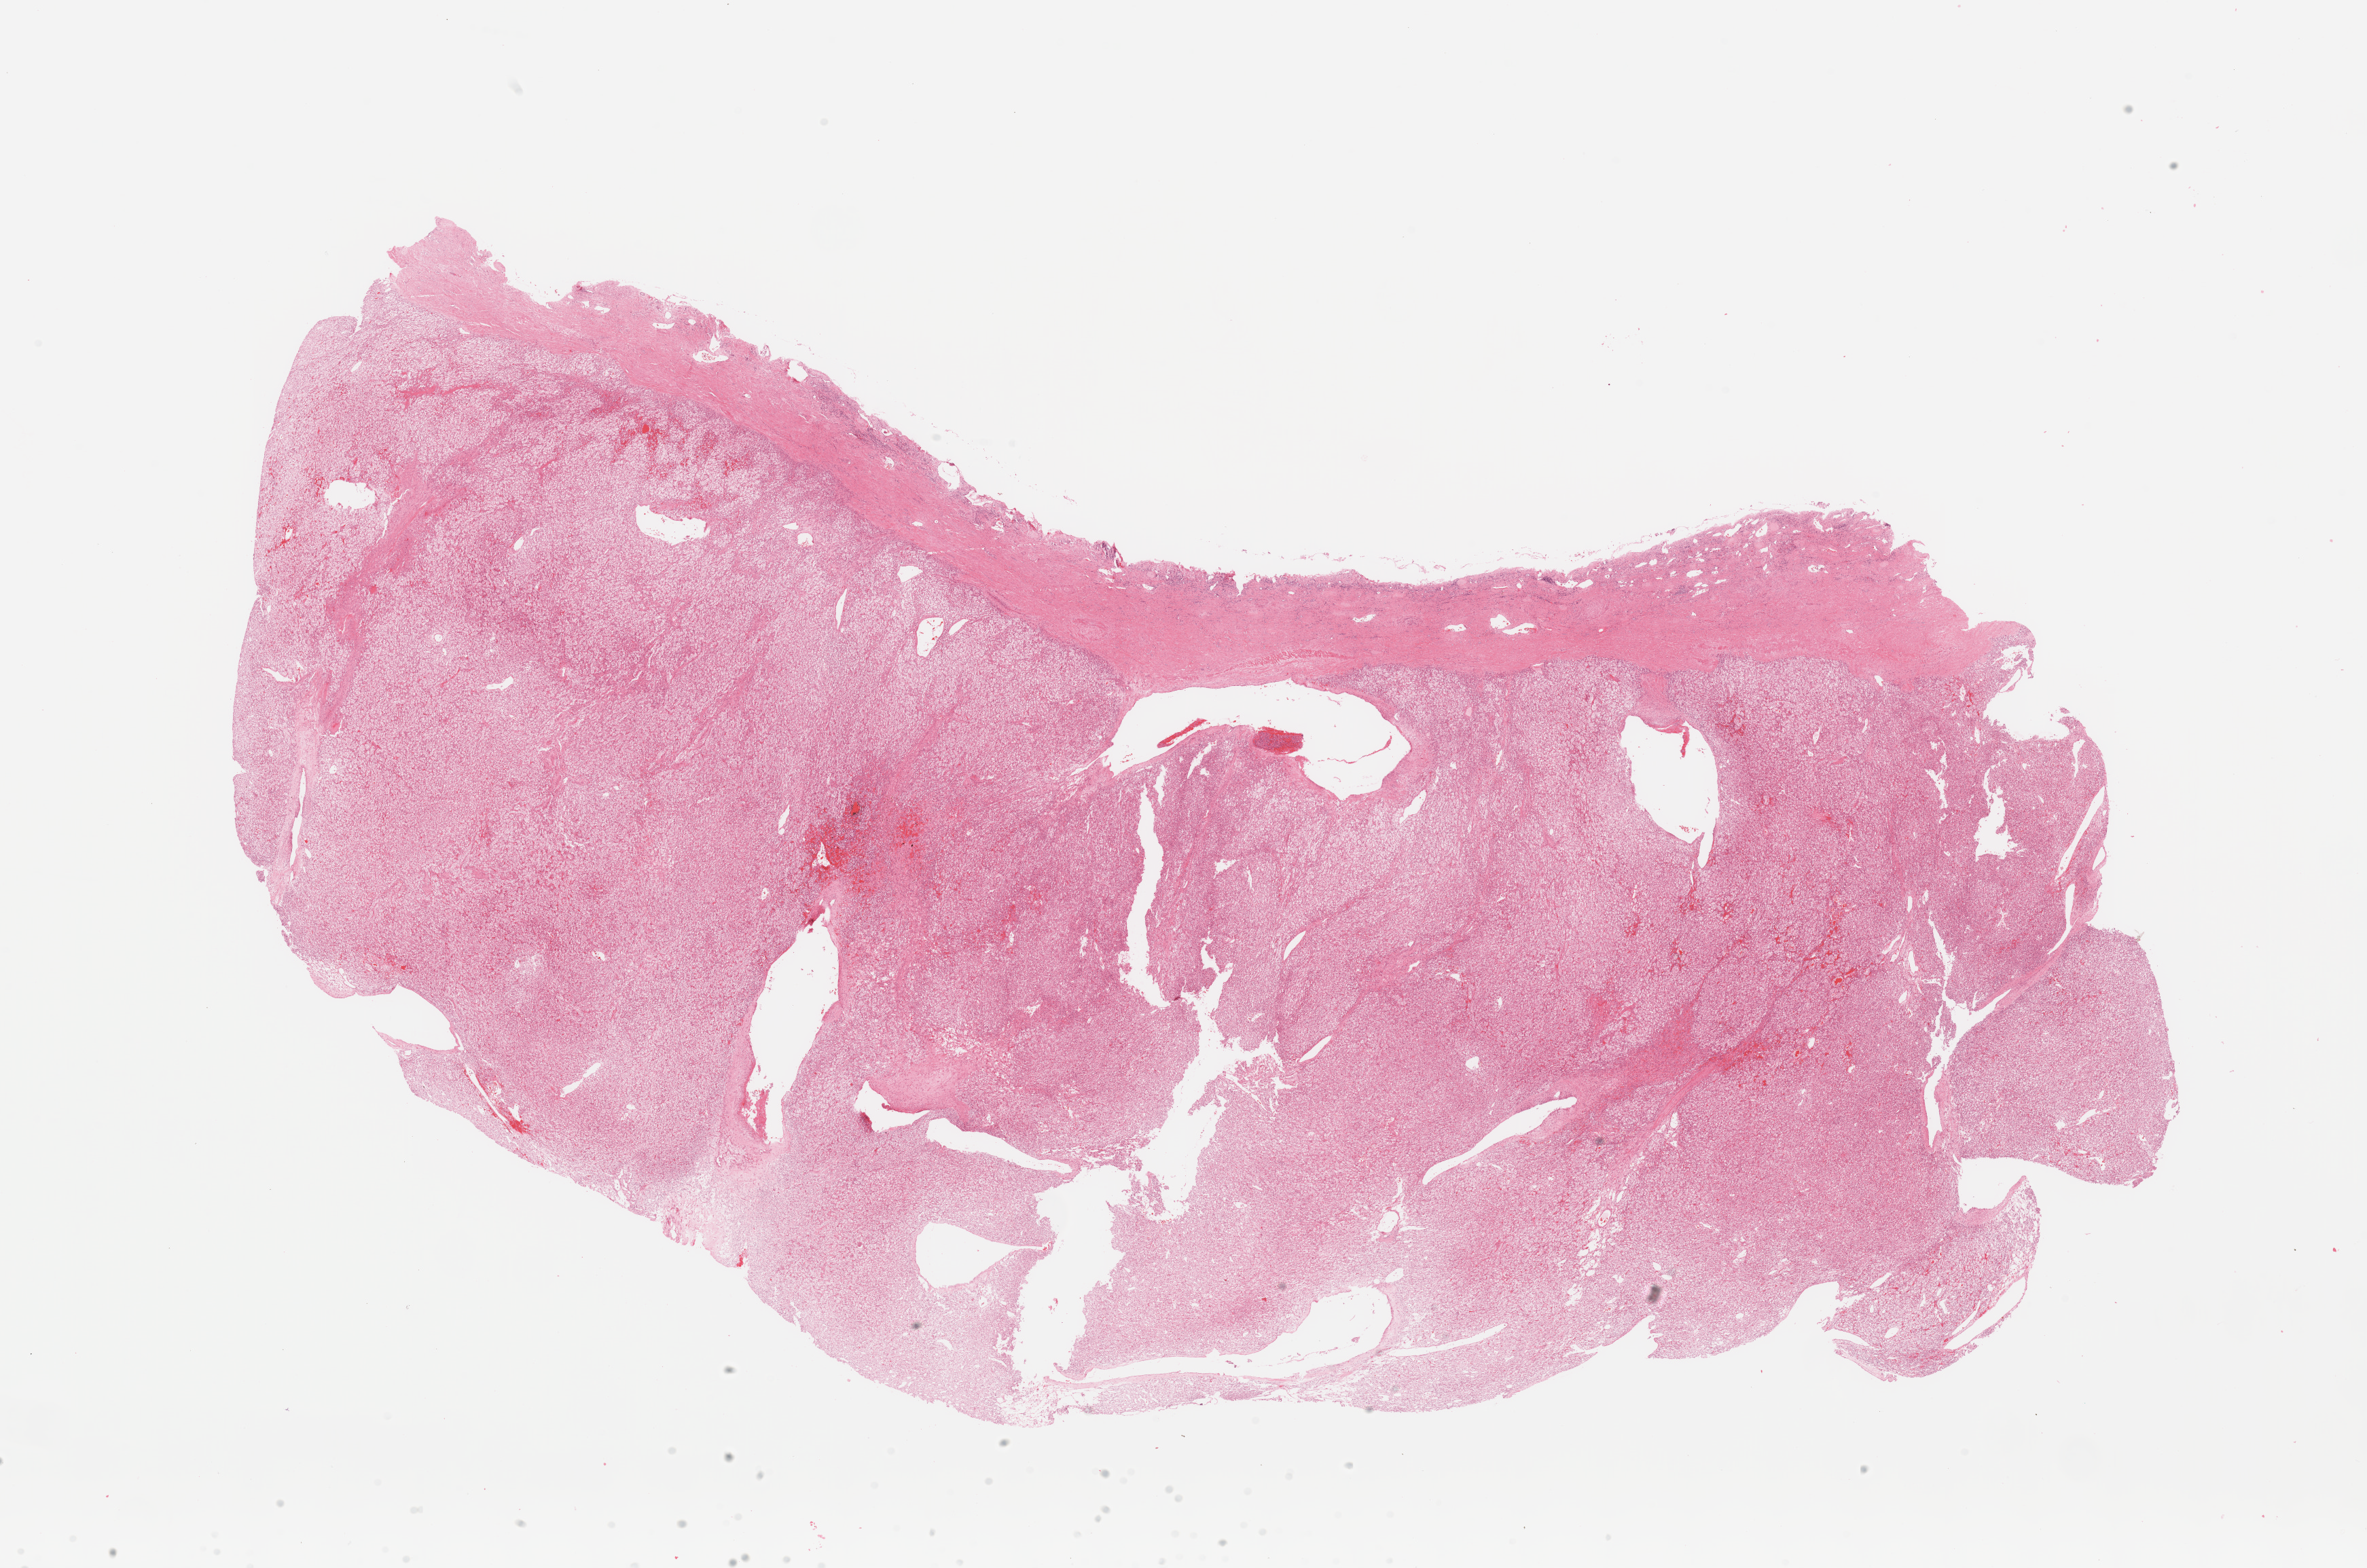
Whole-slide histology image, H&E-stained, a low-resolution overview of the entire scanned area, about 27.6 x 18.3 mm (acquisition: 20x scan), kidney, tumour tissue. 41-year-old female patient. Histologic grade: G2 (moderately differentiated).
Diagnosis: Renal cell carcinoma, NOS. Primary tumour site (as recorded): lower pole.